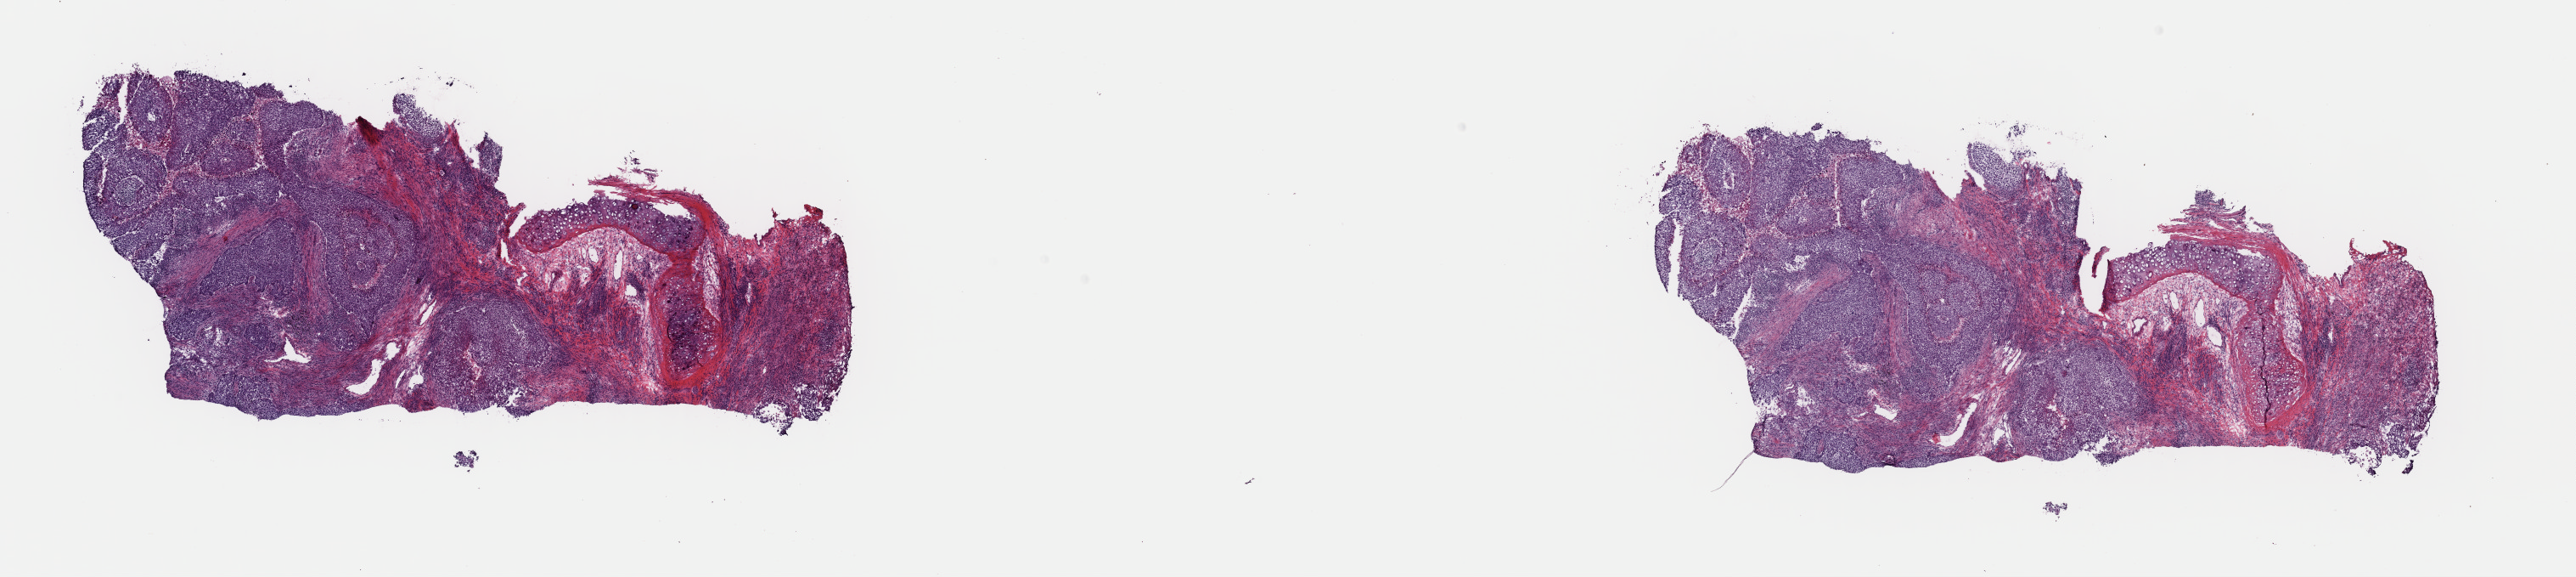
Hematoxylin and eosin (H&E) stained whole-slide image — a low-resolution overview of the entire scanned area, about 24.0 x 5.4 mm (acquisition: 40x scan); frozen section from the top of the tissue portion; primary tumour sample from the lung. Male patient; age at initial diagnosis 73 years. Composition of this section per pathologist review: tumour cells 50%, tumour nuclei 75%.
Pathologic diagnosis: Basaloid squamous cell carcinoma (upper lobe, lung).